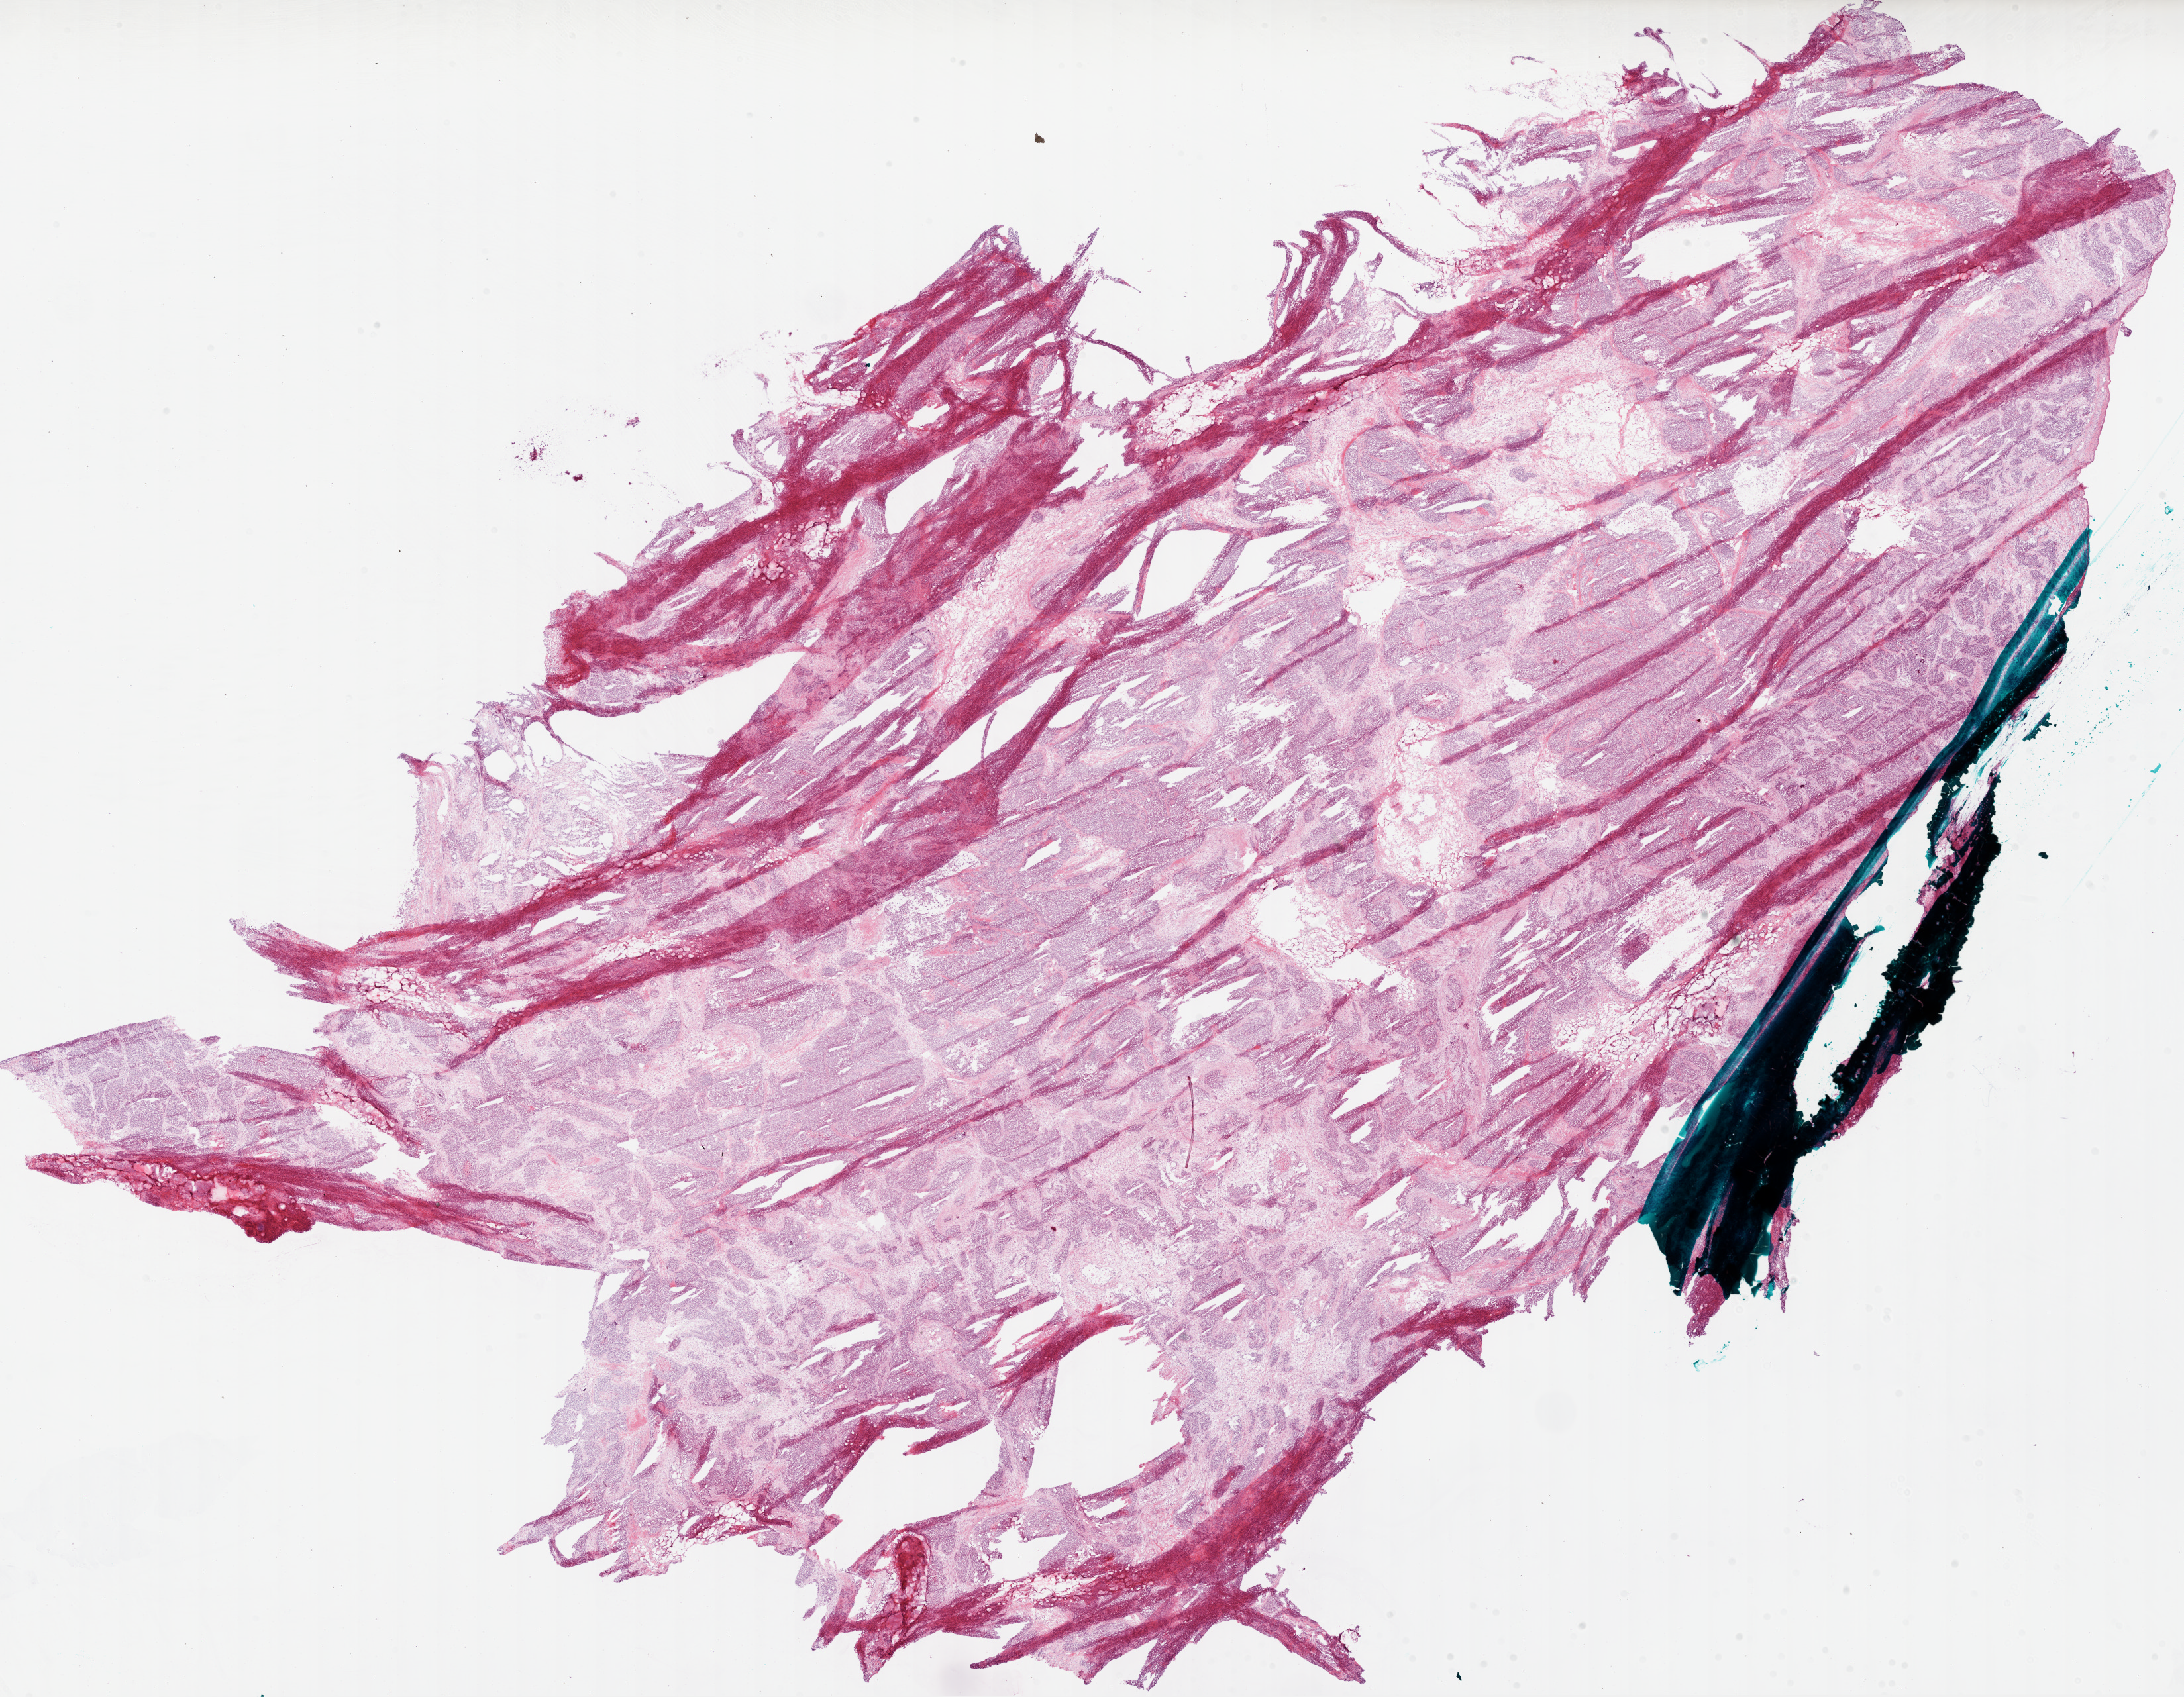
H&E whole-slide image, low-resolution overview of the scanned area, about 26.6 x 20.7 mm (from a 20x scan); frozen section from the bottom of the tissue portion; sample: primary tumour, ovary. Female, age 76 years at initial diagnosis. Composition of this section per pathologist review: tumour cells 70%, tumour nuclei 95%.
Diagnosis: Serous cystadenocarcinoma, NOS.